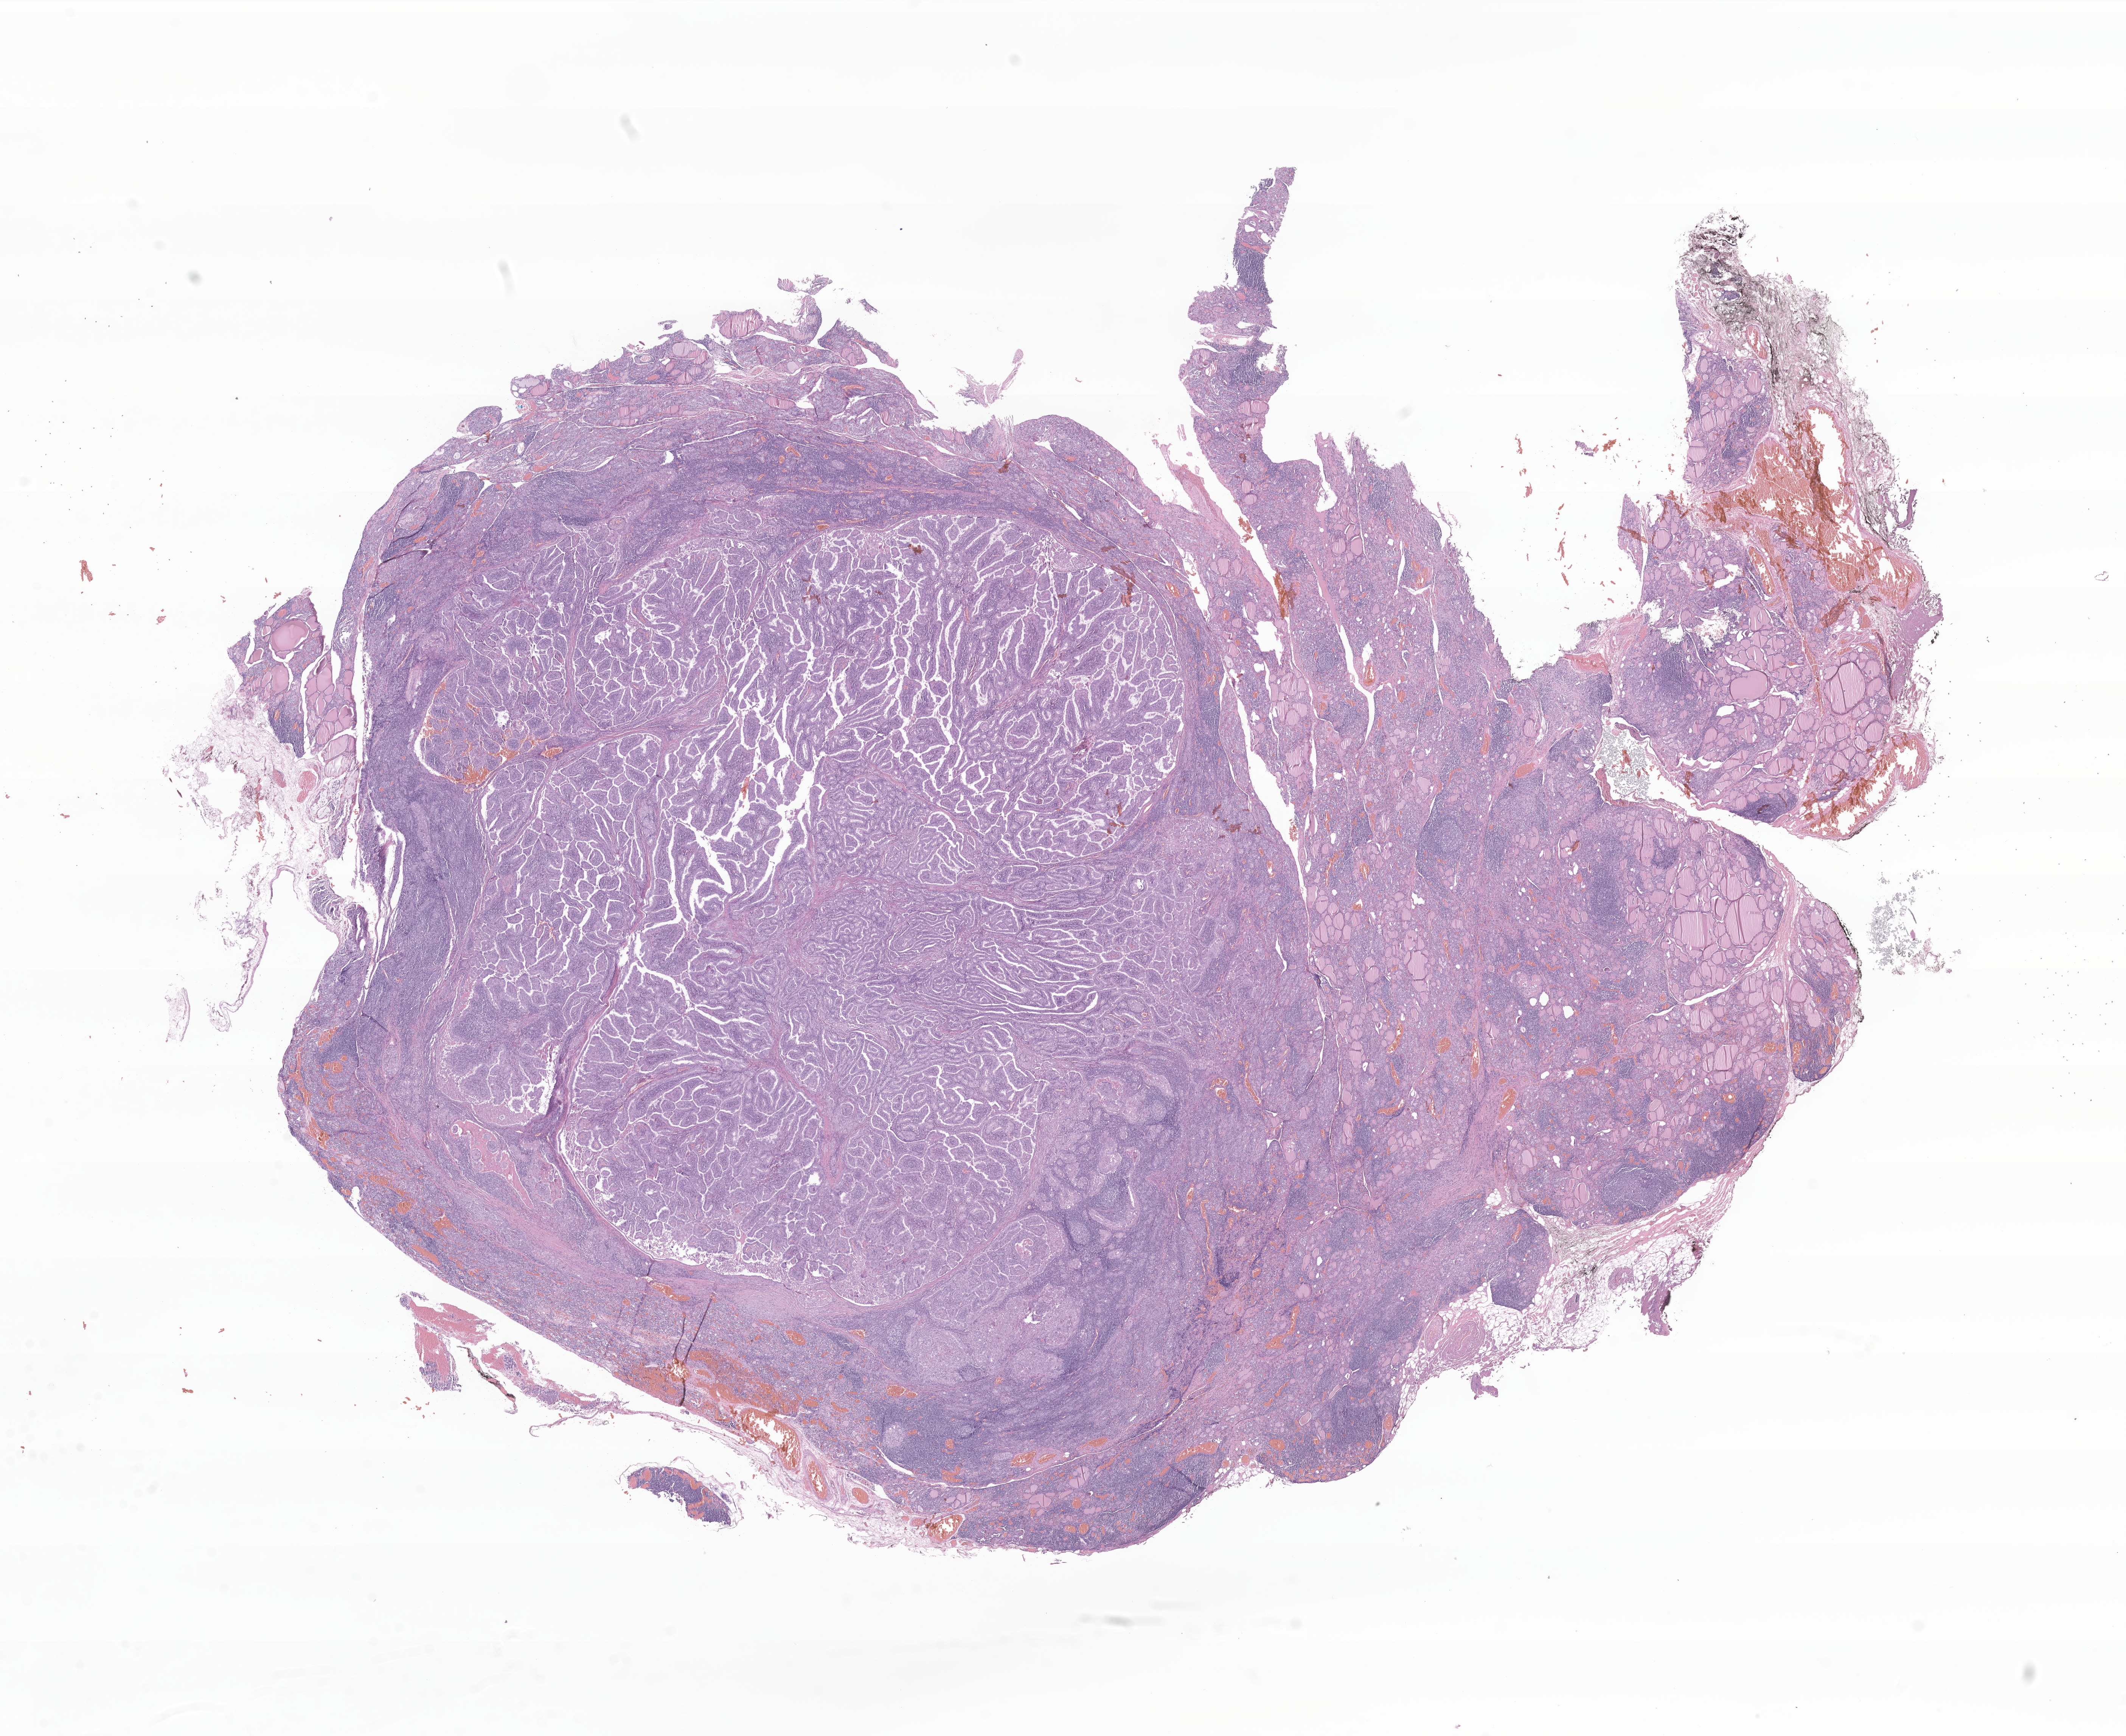
Digitized H&E-stained section of tumor tissue from the thyroid, shown as a low-resolution overview of the whole scanned area (about 23.7 x 19.3 mm); formalin-fixed paraffin-embedded section. Patient: female, age 162 months (13 years 6 months).
Diagnosis (ICD-O-3 morphology term): Papillary carcinoma, NOS.